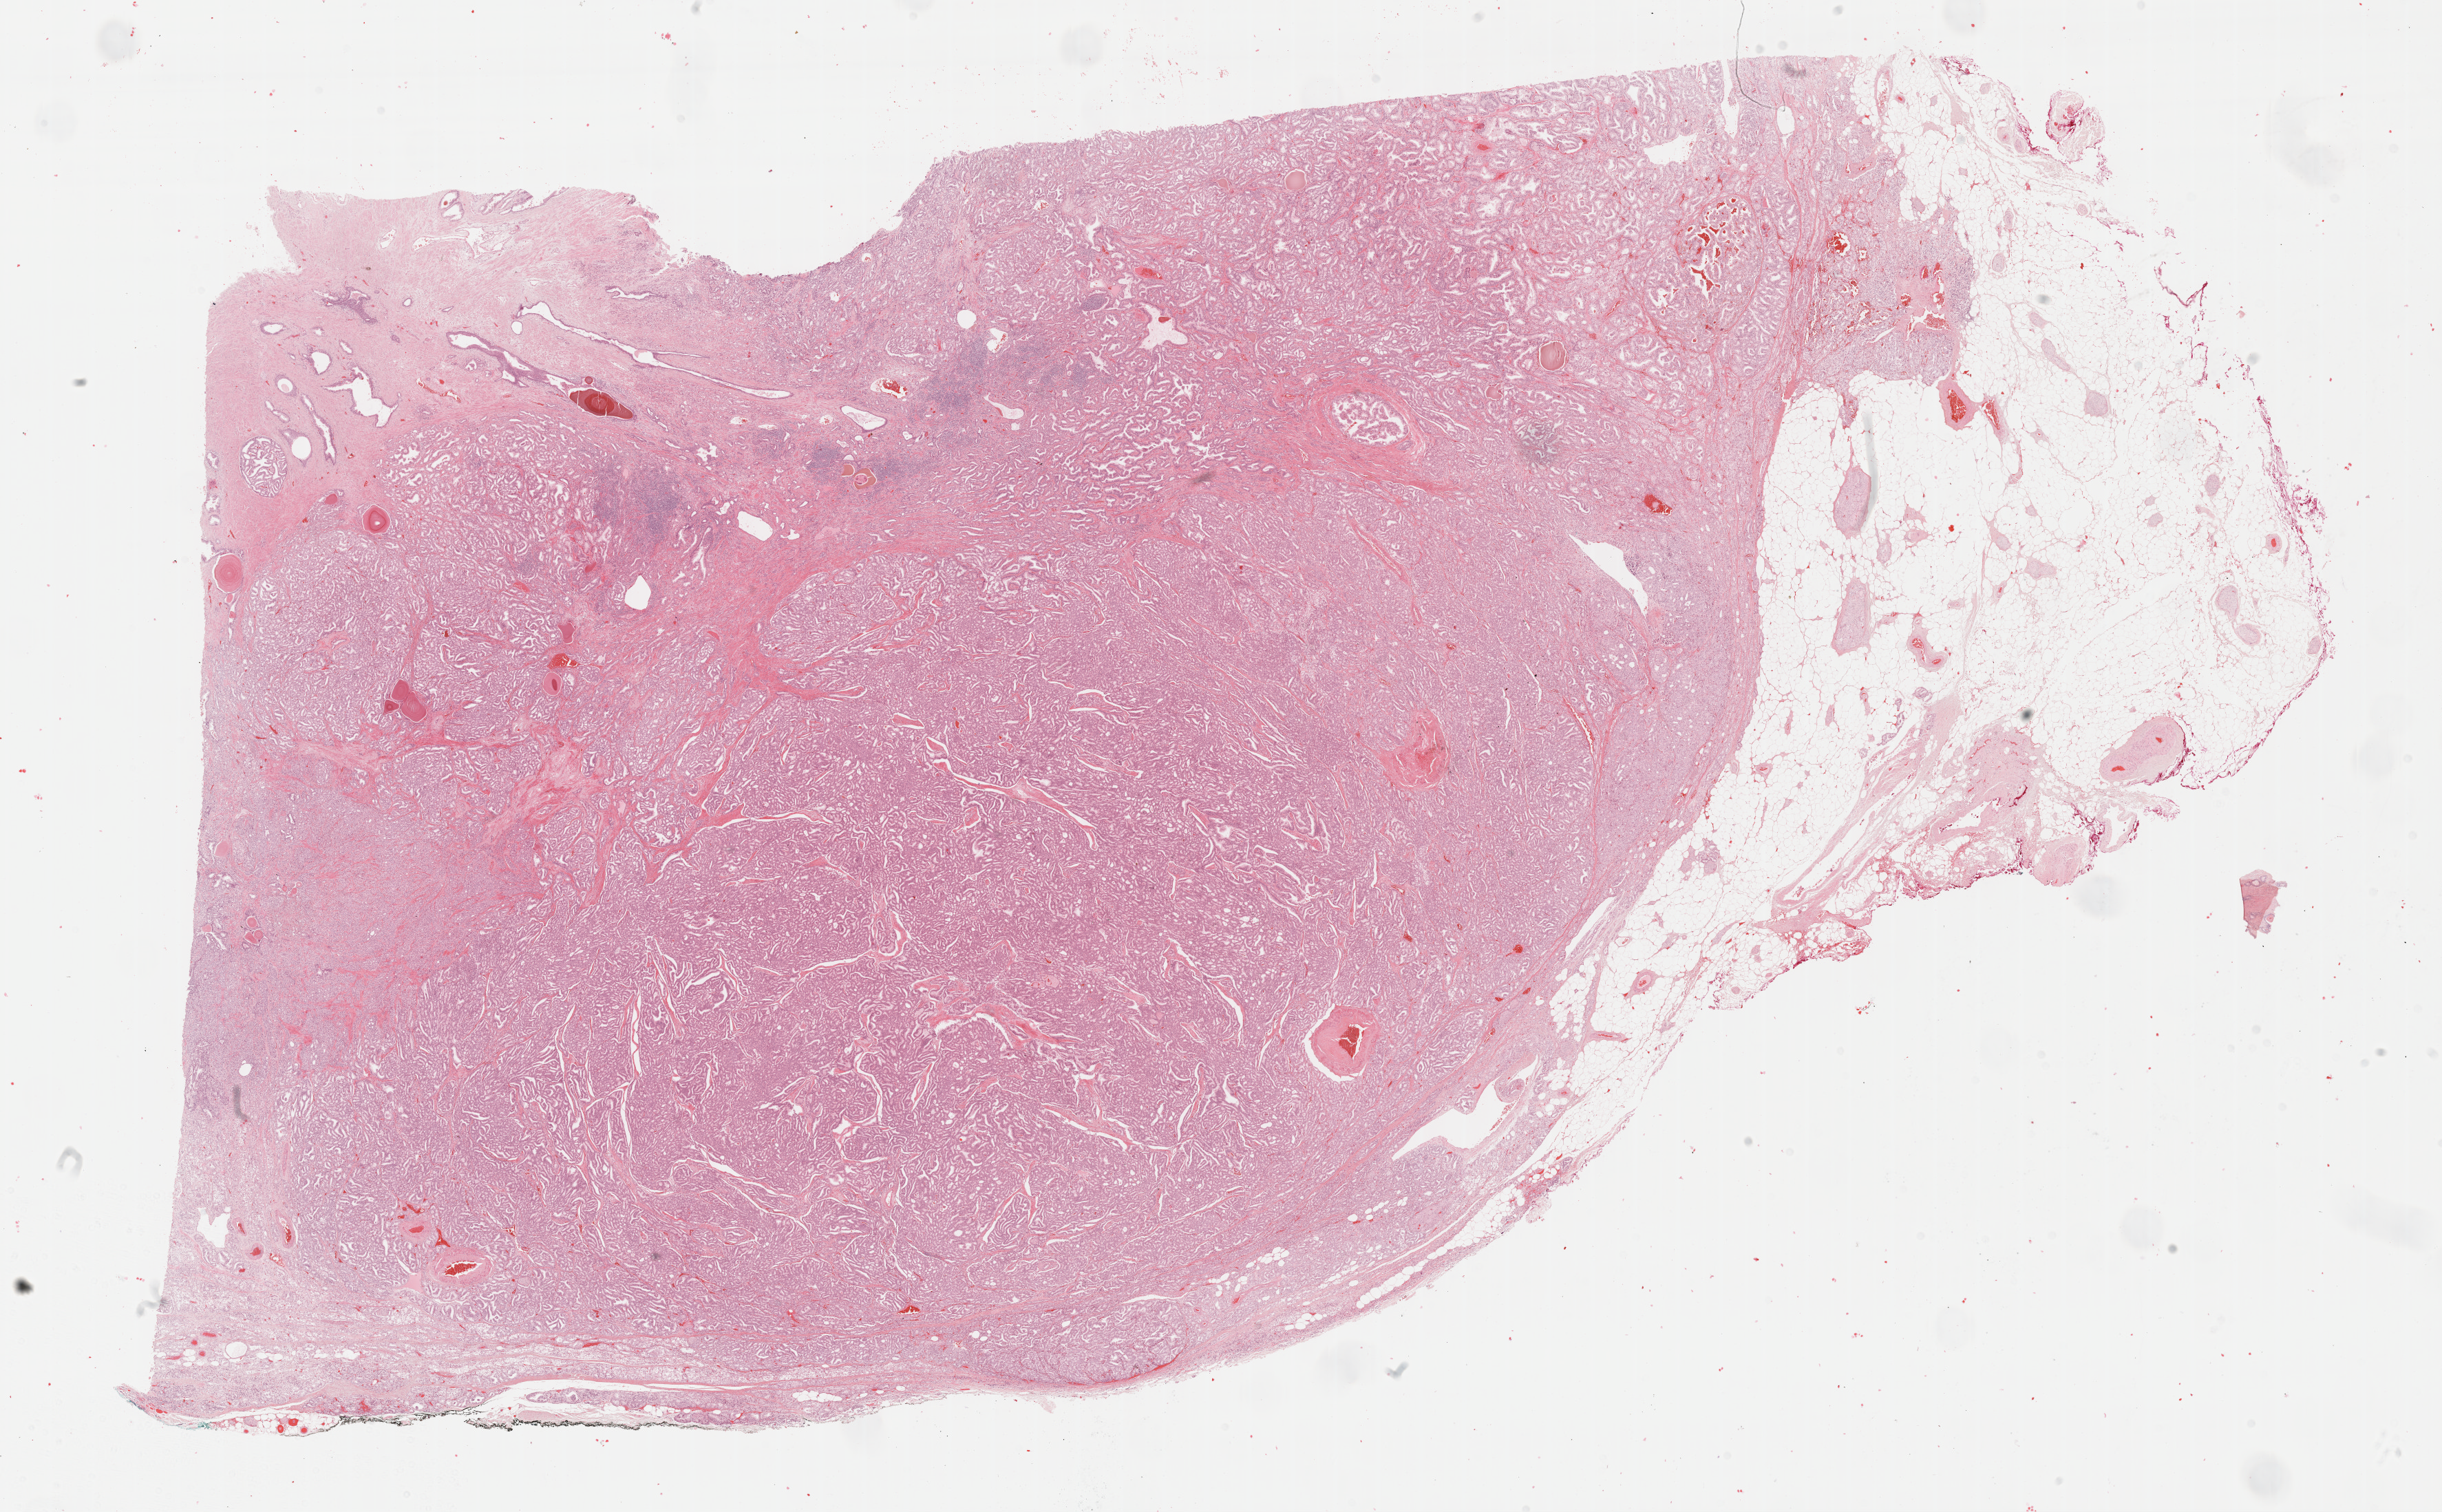
Whole-slide histology image, H&E-stained, whole scanned area (about 28.7 x 17.8 mm, acquisition: 40x scan) shown as a low-resolution overview, formalin-fixed paraffin-embedded (FFPE) diagnostic section, prostate, primary tumour sample. Male patient; age at initial diagnosis 72 years. Gleason score: 8 (4+4).
- laterality: bilateral
- histologic diagnosis: Adenocarcinoma, NOS